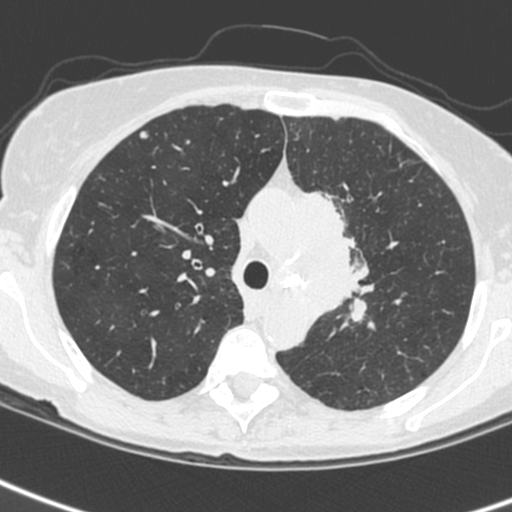
Low-dose screening chest CT, one axial slice. Position 175 of 242 along the scan axis. 120 kVp. Lung window (W 1500 / L -600 HU). 1.3 mm slice thickness. 512 × 512 image matrix, field of view 284 × 284 mm.
Outlined on this slice (outlined manually by an expert reader):
- lesion 3 (tumor, upper lobe of left lung): bounding box [x1, y1, x2, y2] px = [301, 191, 356, 316]